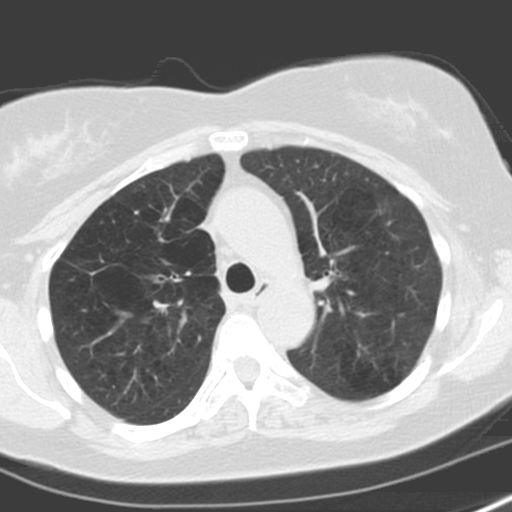
Axial slice from a low-dose chest CT screening exam; first (baseline) screen; lung window (W 1500 / L -600 HU); 3.2 mm slice thickness; 120 kVp; slice 55 of 173 in the series; 512 × 512 image matrix, field of view 278 × 278 mm. Female, age 57 years at enrolment. Former smoker at enrolment.
Expert reader's lesion annotation, bounding box <358,195,401,228> (left, top, right, bottom; pixels). No non-calcified nodule or mass ≥4 mm was recorded by the screening reader at this exam. Later outcome: lung cancer diagnosed 503 days after this screen (after the second annual screen) — adenocarcinoma, NOS, left upper lobe, moderately differentiated (G2), stage IA (AJCC 6th edition), 18 mm at pathology.